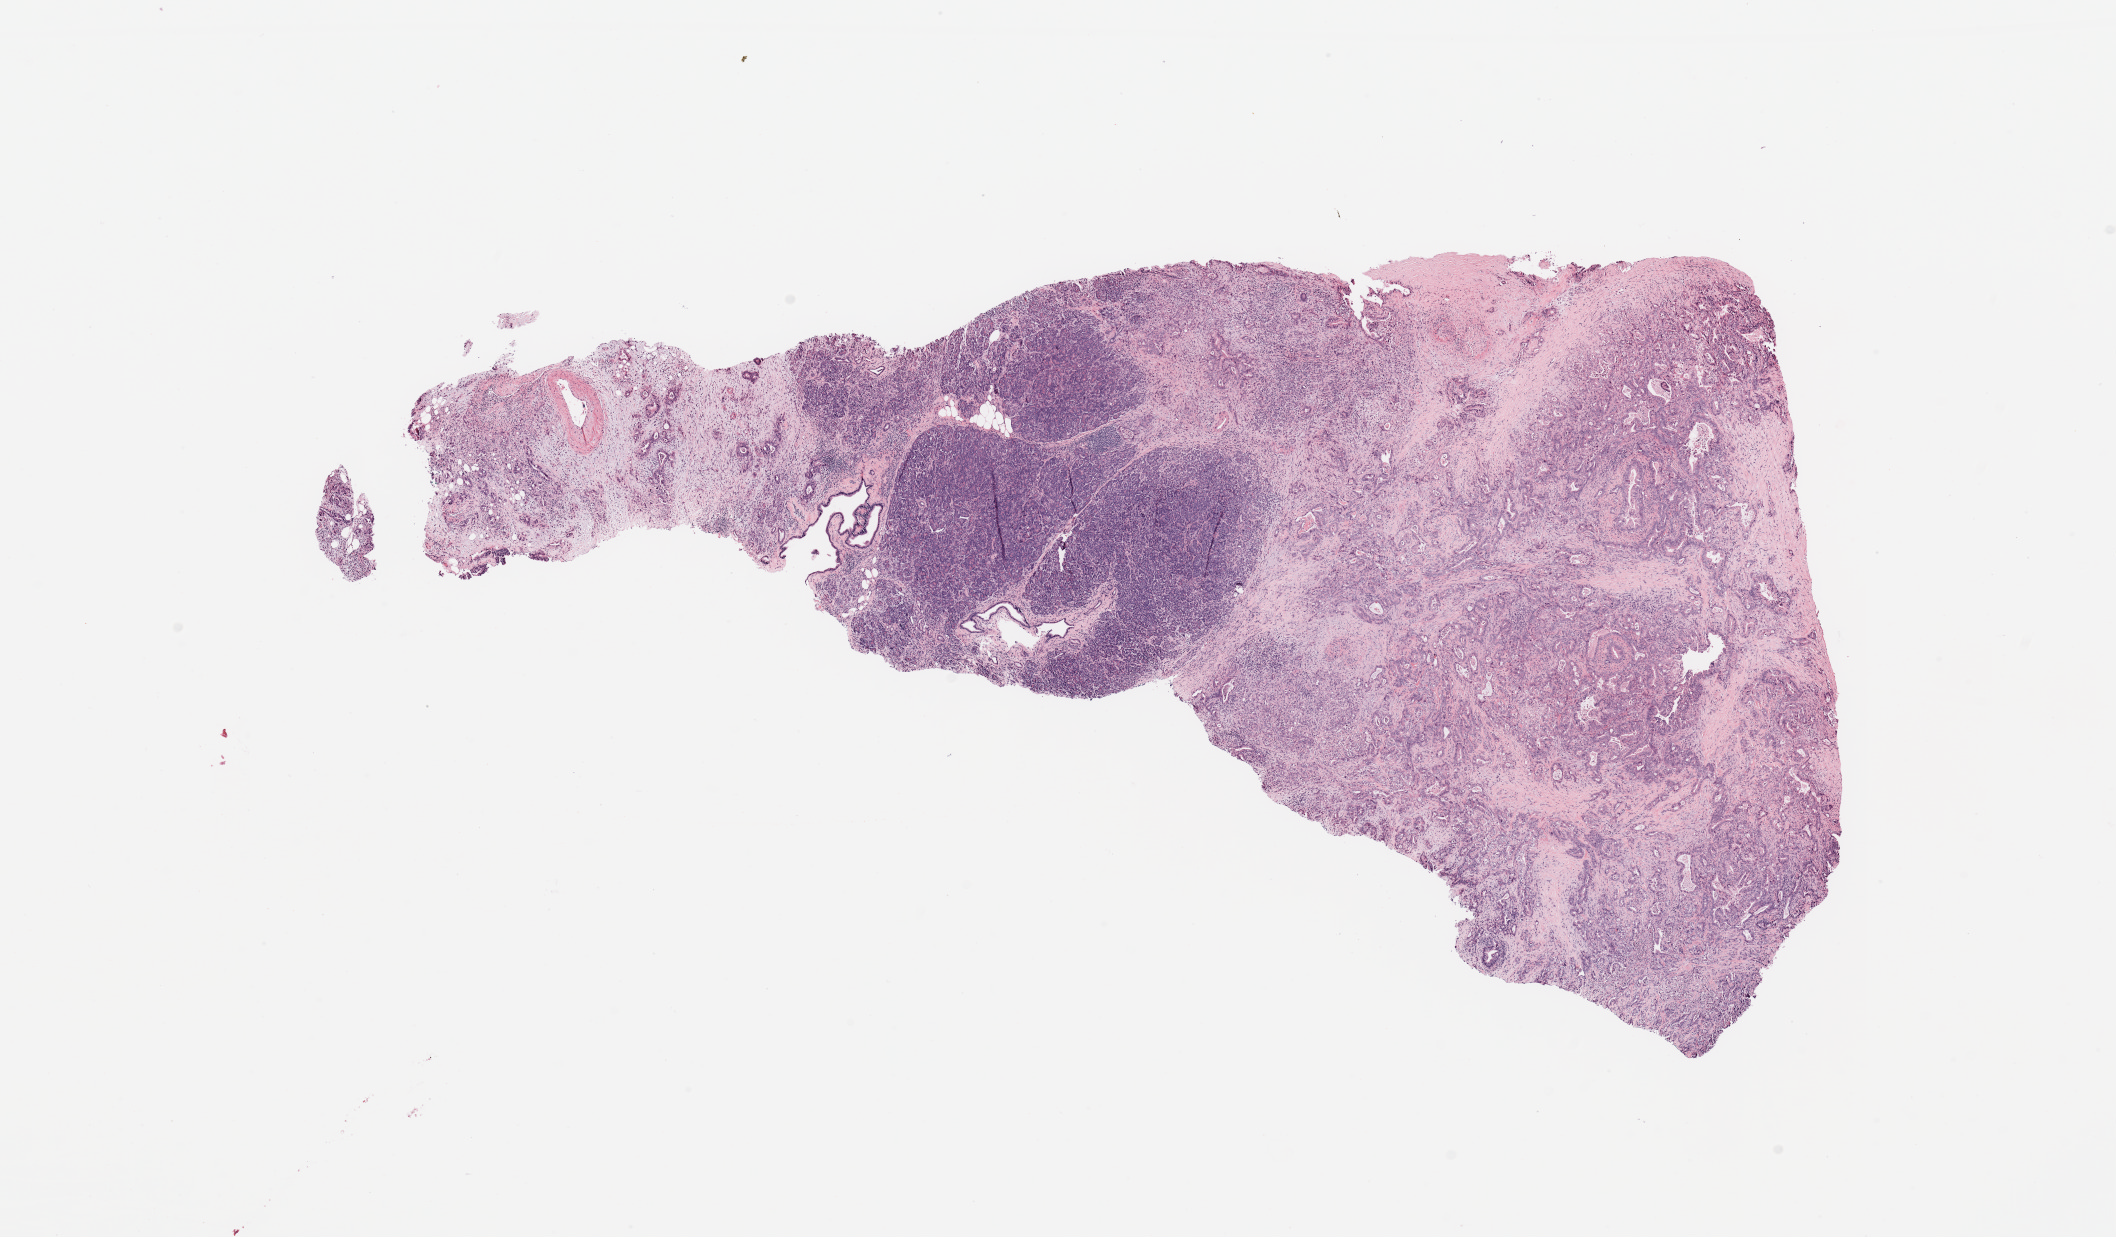
H&E-stained whole-slide image, shown as a low-resolution overview of the whole scanned area (about 16.7 x 9.8 mm, from a 20x scan), tumour tissue sample, sampled site: pancreas. Female, 73 y/o. Histologic grade: G2 (moderately differentiated). Composition of this section per pathologist review: tumour nuclei 60%, necrosis 5%.
* diagnosis: Infiltrating duct carcinoma, NOS
* primary tumour site (as recorded): head